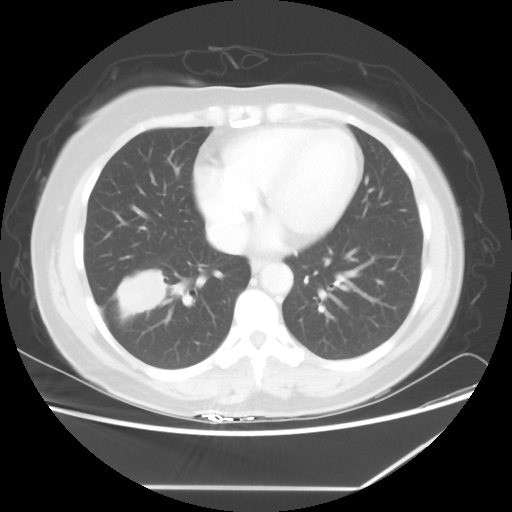
Chest CT, one axial slice; slice 24 of 60 in the series (ordered by position); reconstruction kernel STANDARD; 100 kVp; lung window (W 1500 / L -600 HU); 5 mm slice thickness; 512 × 512 image matrix. Female patient, age 42 years. From the clinical record (not read from this slice): clinical TNM (as recorded): T2 N1 M0.
Outlined on this slice (bounding box drawn by a radiologist):
- lung tumour (recorded histology: adenocarcinoma): box from (x=116, y=266) to (x=168, y=318) px